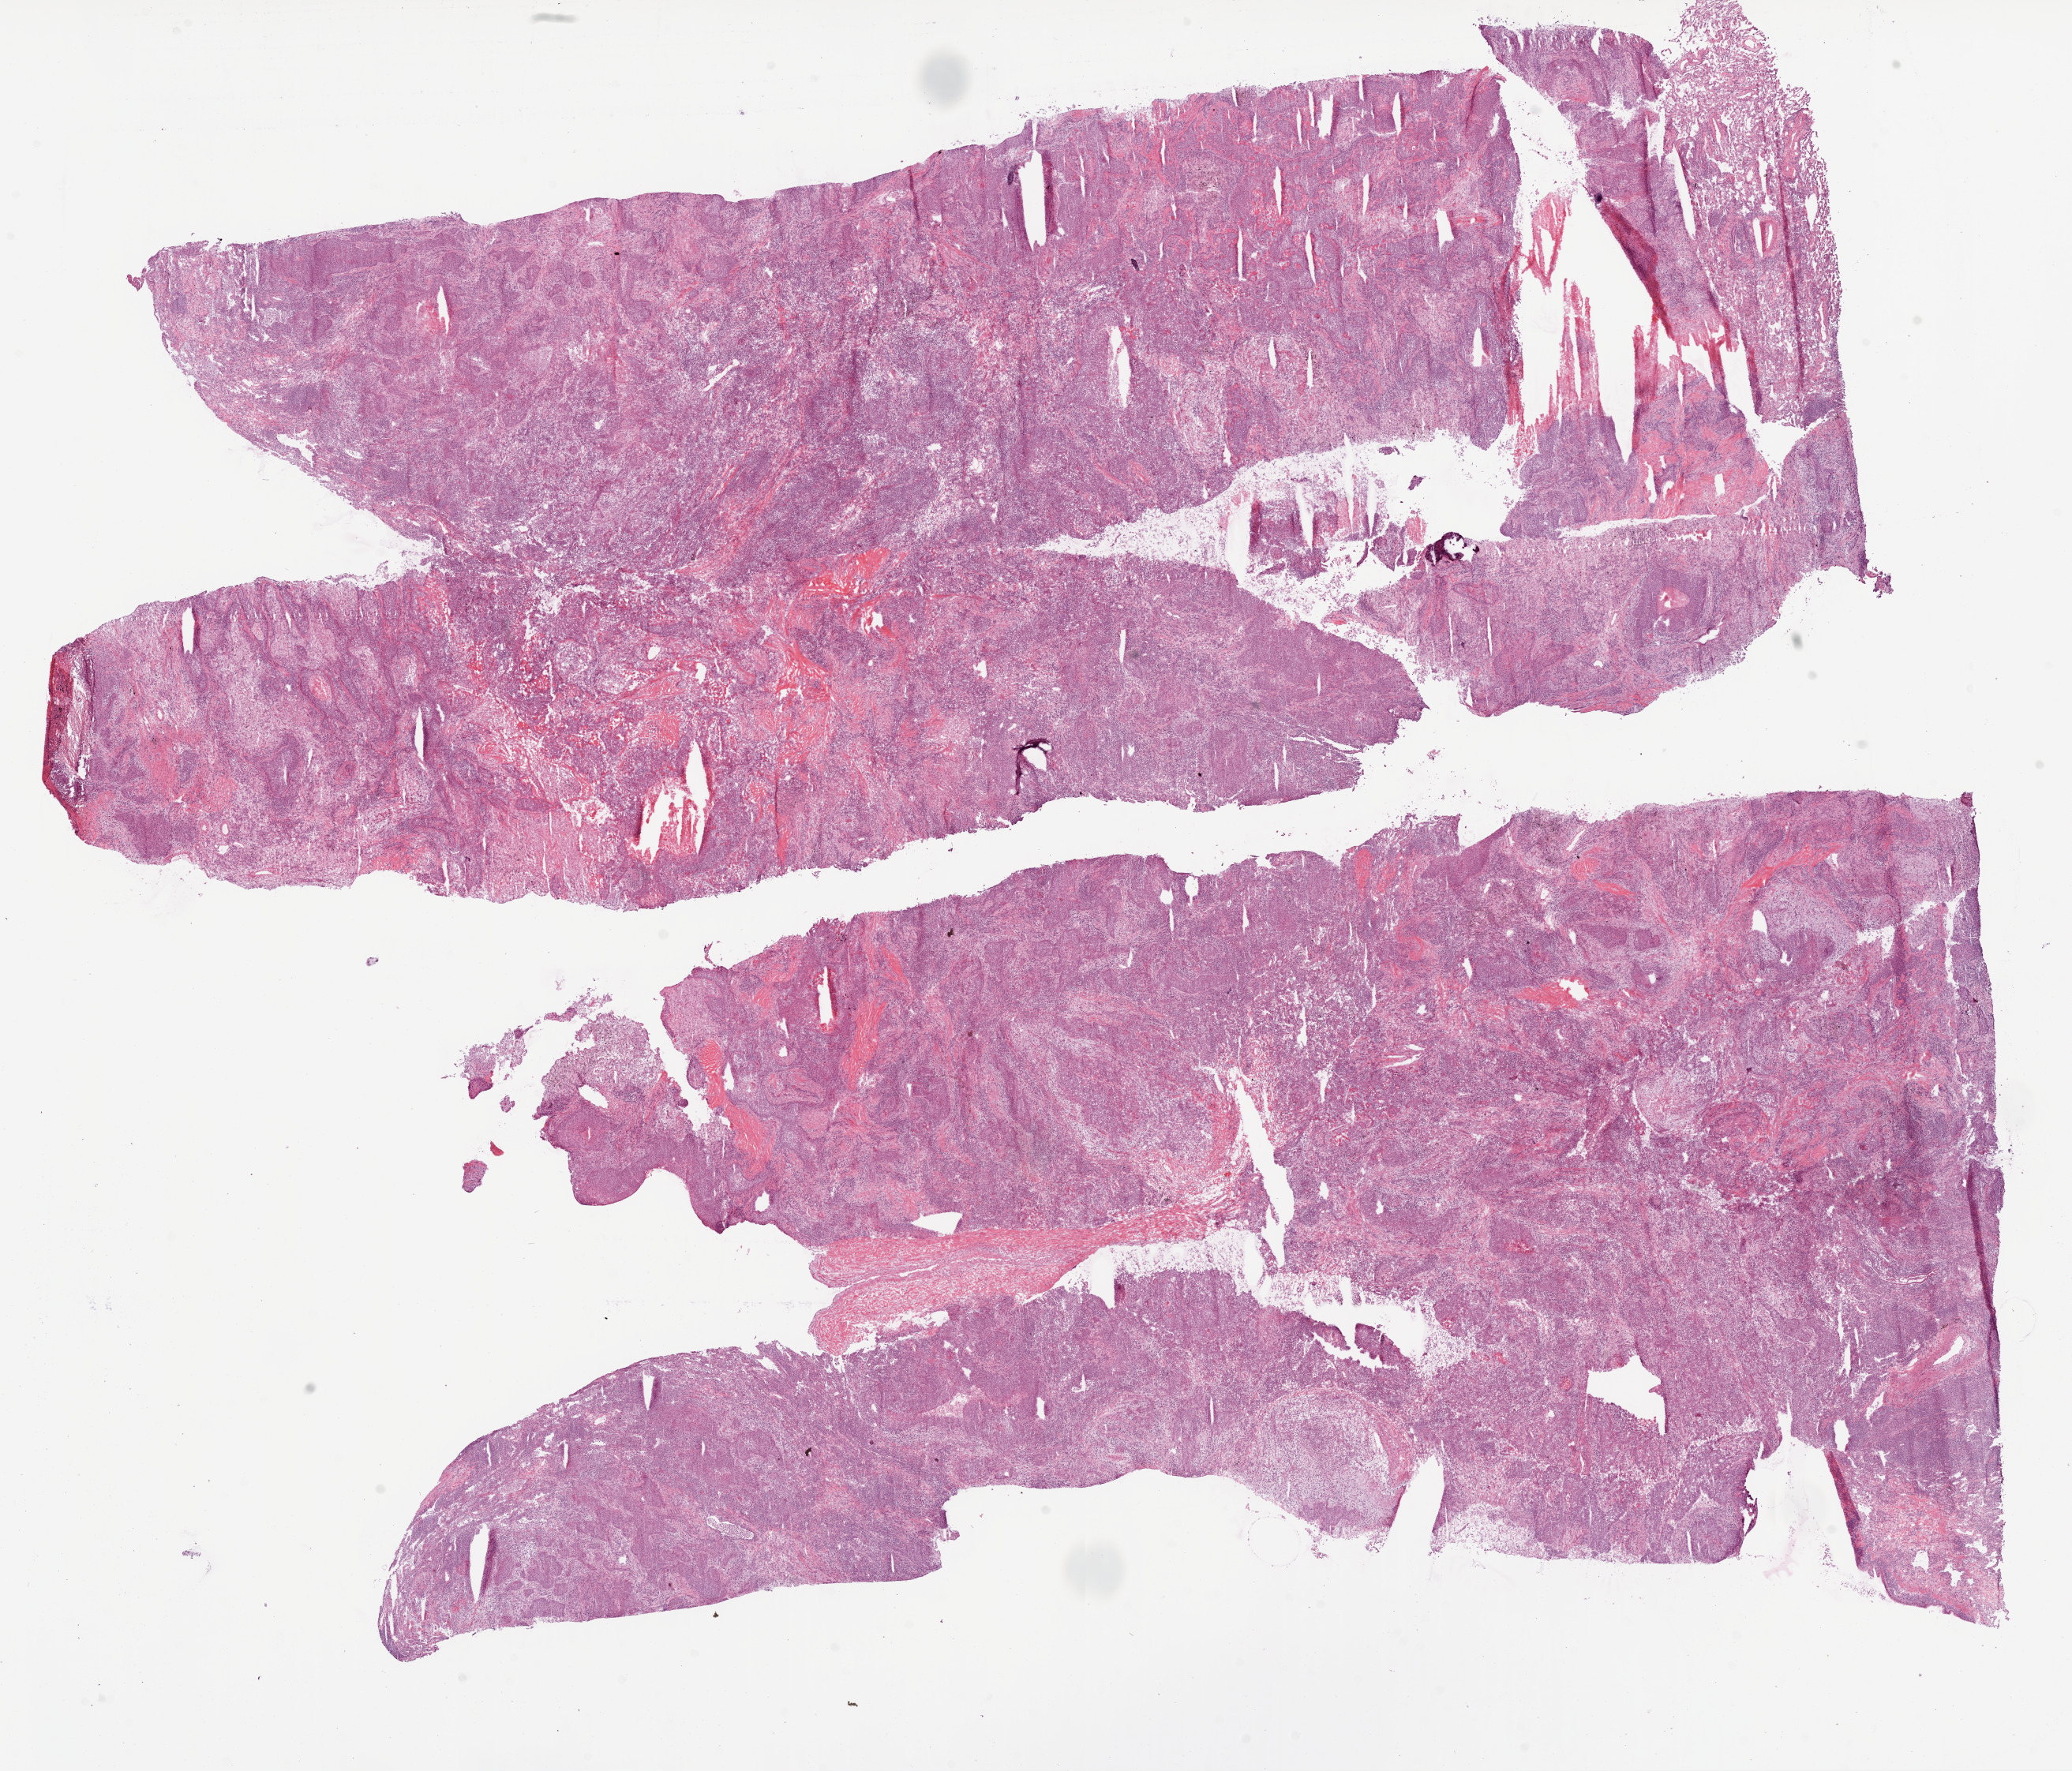
H&E-stained whole-slide image, a low-resolution overview of the entire scanned area, about 21.1 x 18.0 mm; frozen section from the bottom of the tissue portion; sample: primary tumour, lung. Female patient; age at initial diagnosis 81 years. Slide review estimates, as recorded: tumour cells 65%, tumour nuclei 75%, normal cells 5%, stromal cells 25%, necrosis 5%.
* diagnosis: Squamous cell carcinoma, NOS (lower lobe, lung)
* AJCC pathologic stage: IIIA